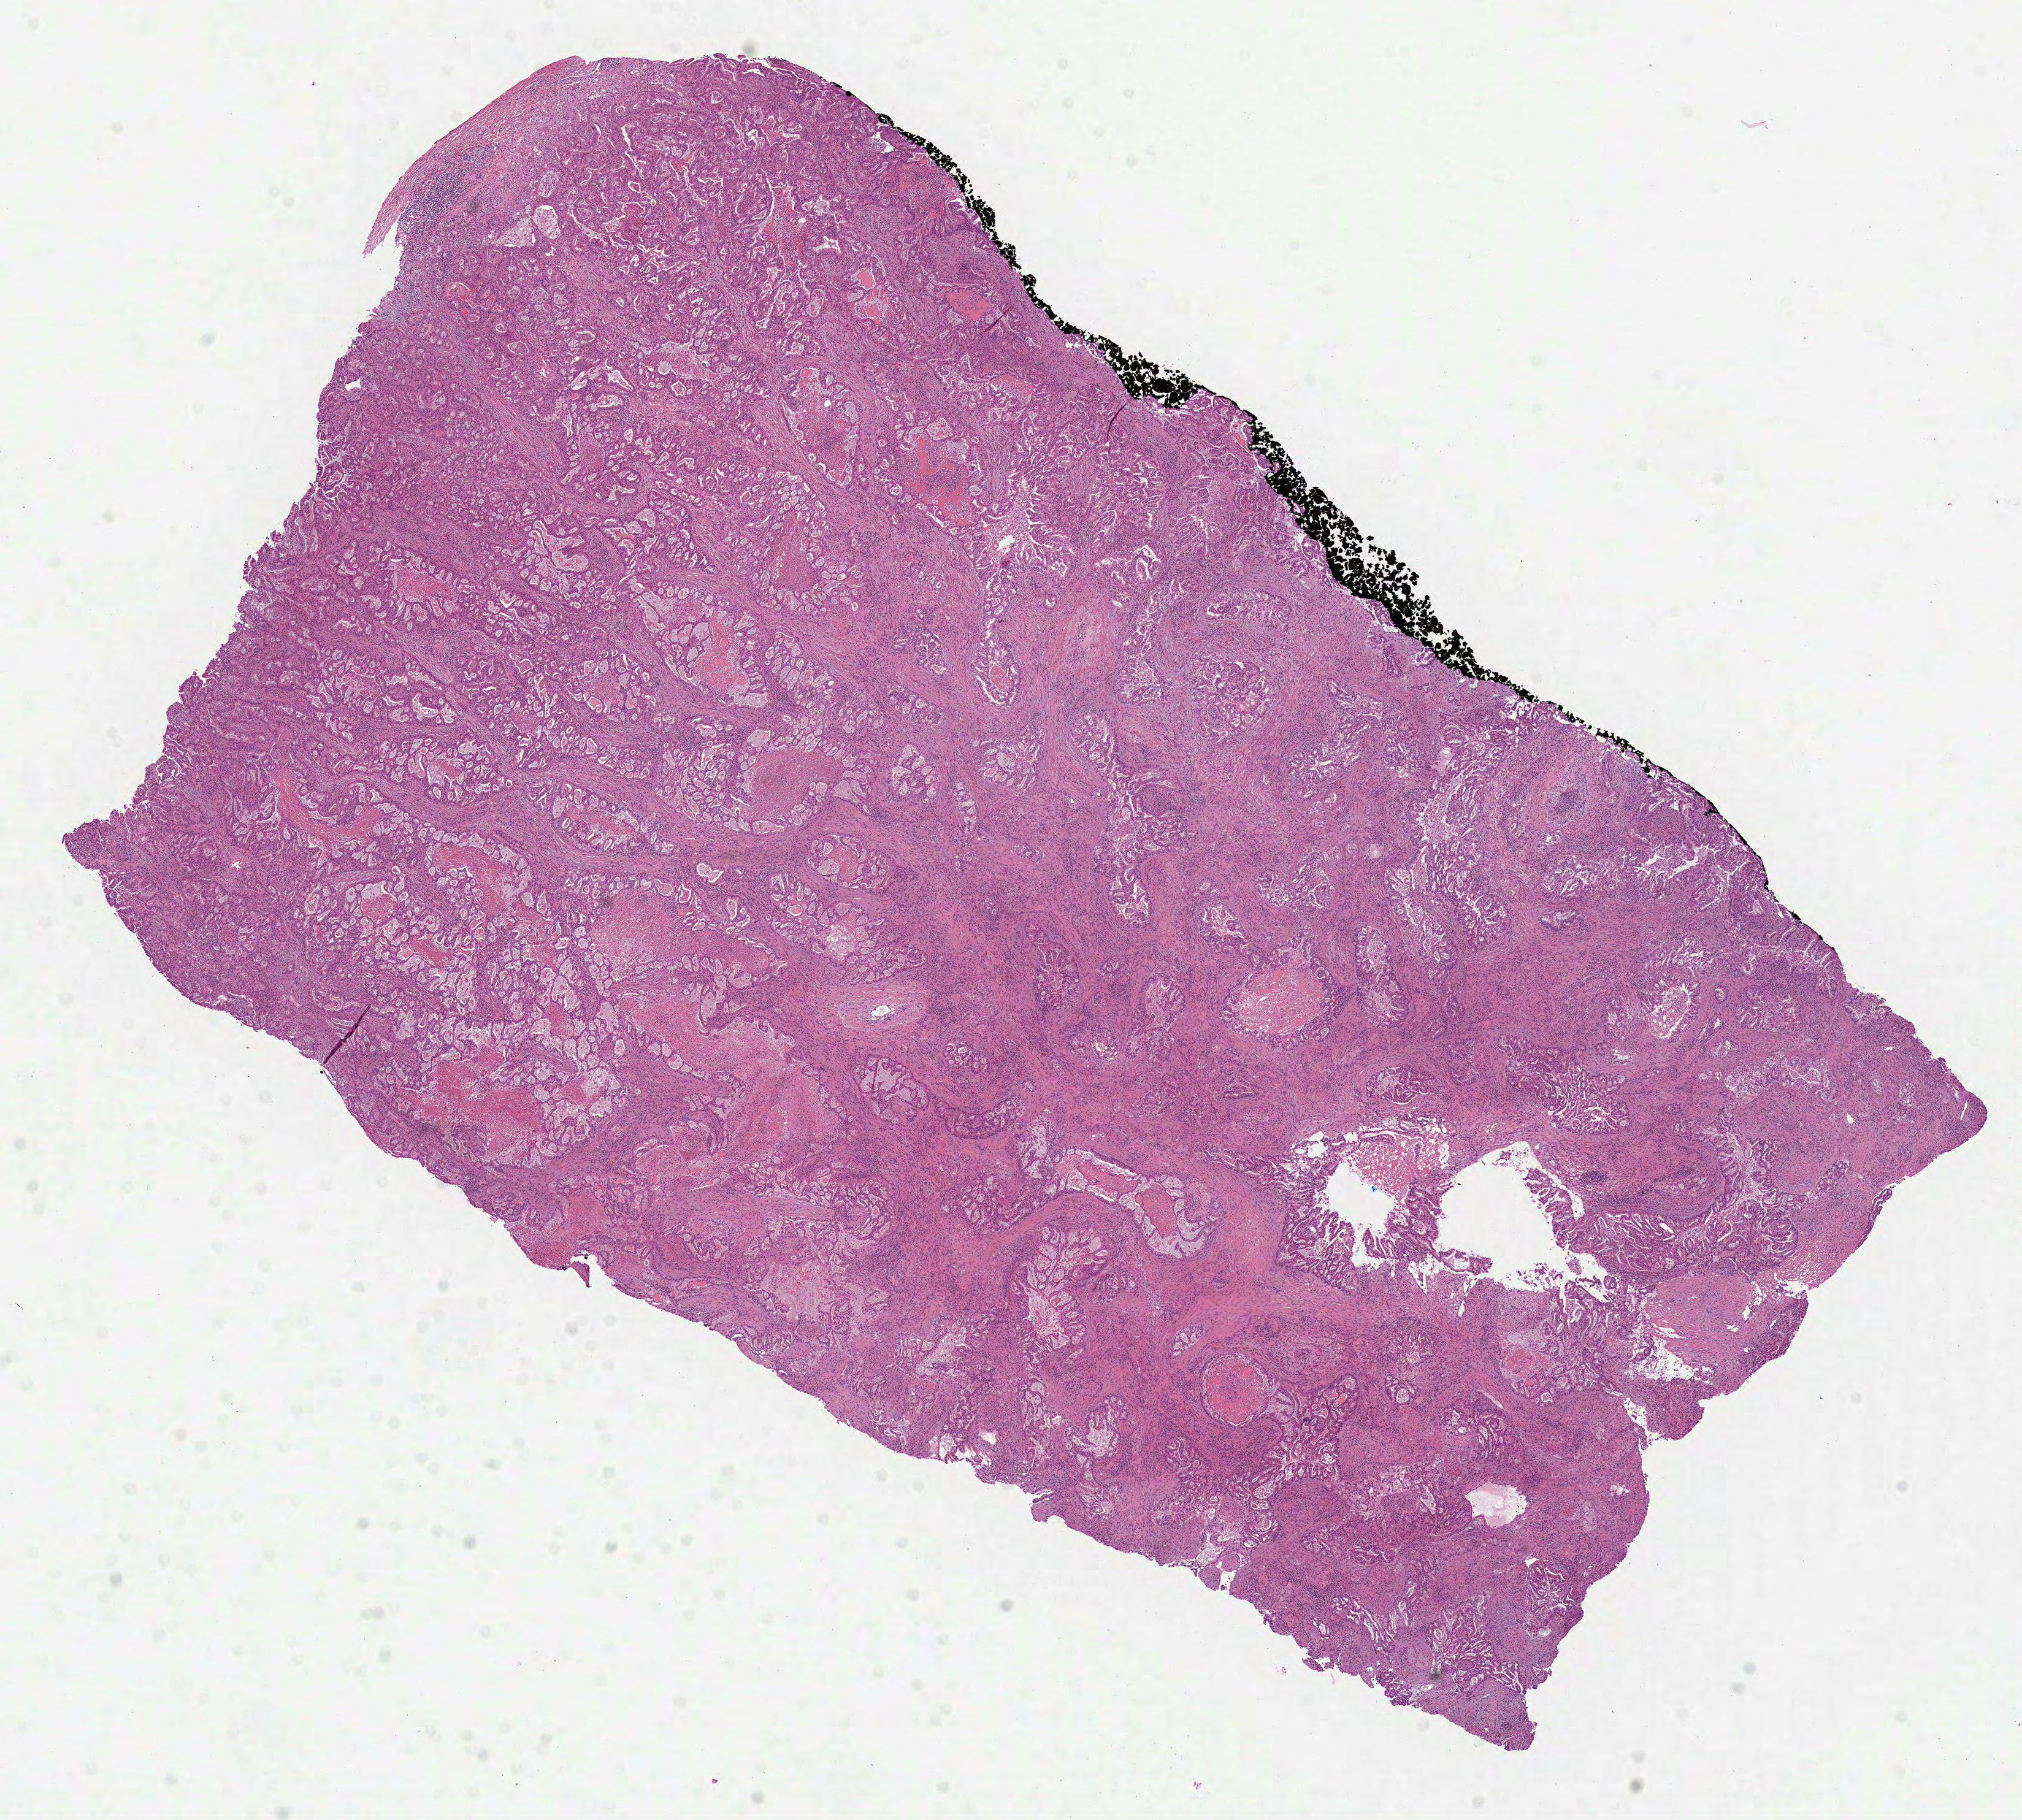
Whole-slide histology image, H&E-stained — low-resolution overview of the scanned area, about 13.3 x 12.0 mm (slide scanned at 40x), formalin-fixed paraffin-embedded (FFPE) diagnostic section, lung, primary tumour sample. Male patient; age at initial diagnosis 76 years.
Diagnosis: Adenocarcinoma, NOS. Laterality: right. AJCC pathologic stage: IB (7th edition).